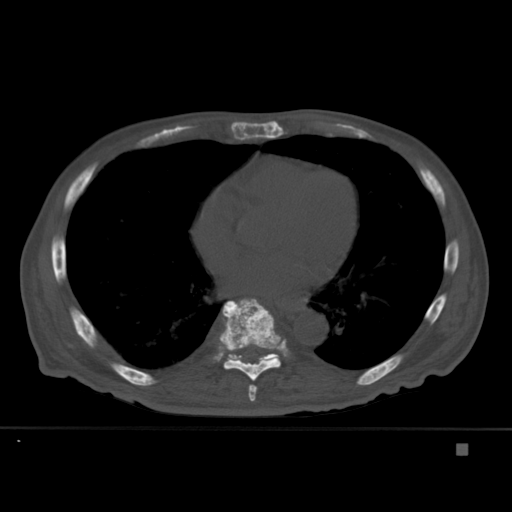
CT including the spine, one axial slice; position 261 of 451 along the scan axis; bone window (W 1800 / L 400 HU); 1.5 mm slice thickness; 512 × 512 image matrix. Patient: male, 75 years. Case-level facts recorded for this patient, not image findings: primary cancer: prostate.
Annotated regions visible in this slice (semi-automatically segmented with operator editing):
- T7 vertebra: bounding box [x1, y1, x2, y2] px = [248, 385, 257, 402]
- T8 vertebra: [219, 298, 281, 381]
- T9 vertebra: [224, 353, 279, 363]